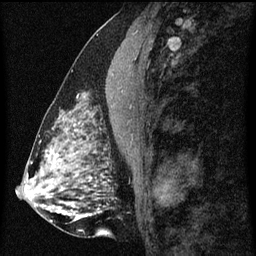
Breast MRI (dynamic contrast-enhanced), one sagittal slice; position 27 of 60 along the scan axis; dynamic contrast-enhanced series, image 2 of 3 at this slice position (ordered by acquisition); 1.5 T; TE 4.2 ms, TR 8 ms; 256 × 256 image matrix, field of view 180 × 180 mm. Patient: female, 51 years.
Annotated regions visible in this slice (semi-automatic segmentation, software-assisted and operator-edited):
- analysis volume of interest (the breast-tissue region the enhancement analysis was run in; not a lesion): bounding box (x1, y1, x2, y2) in pixels: (61, 78, 96, 129)
- tumour enhancement mask (voxels above the 70 % enhancement threshold inside the analysis volume of interest): (74, 94, 87, 125)